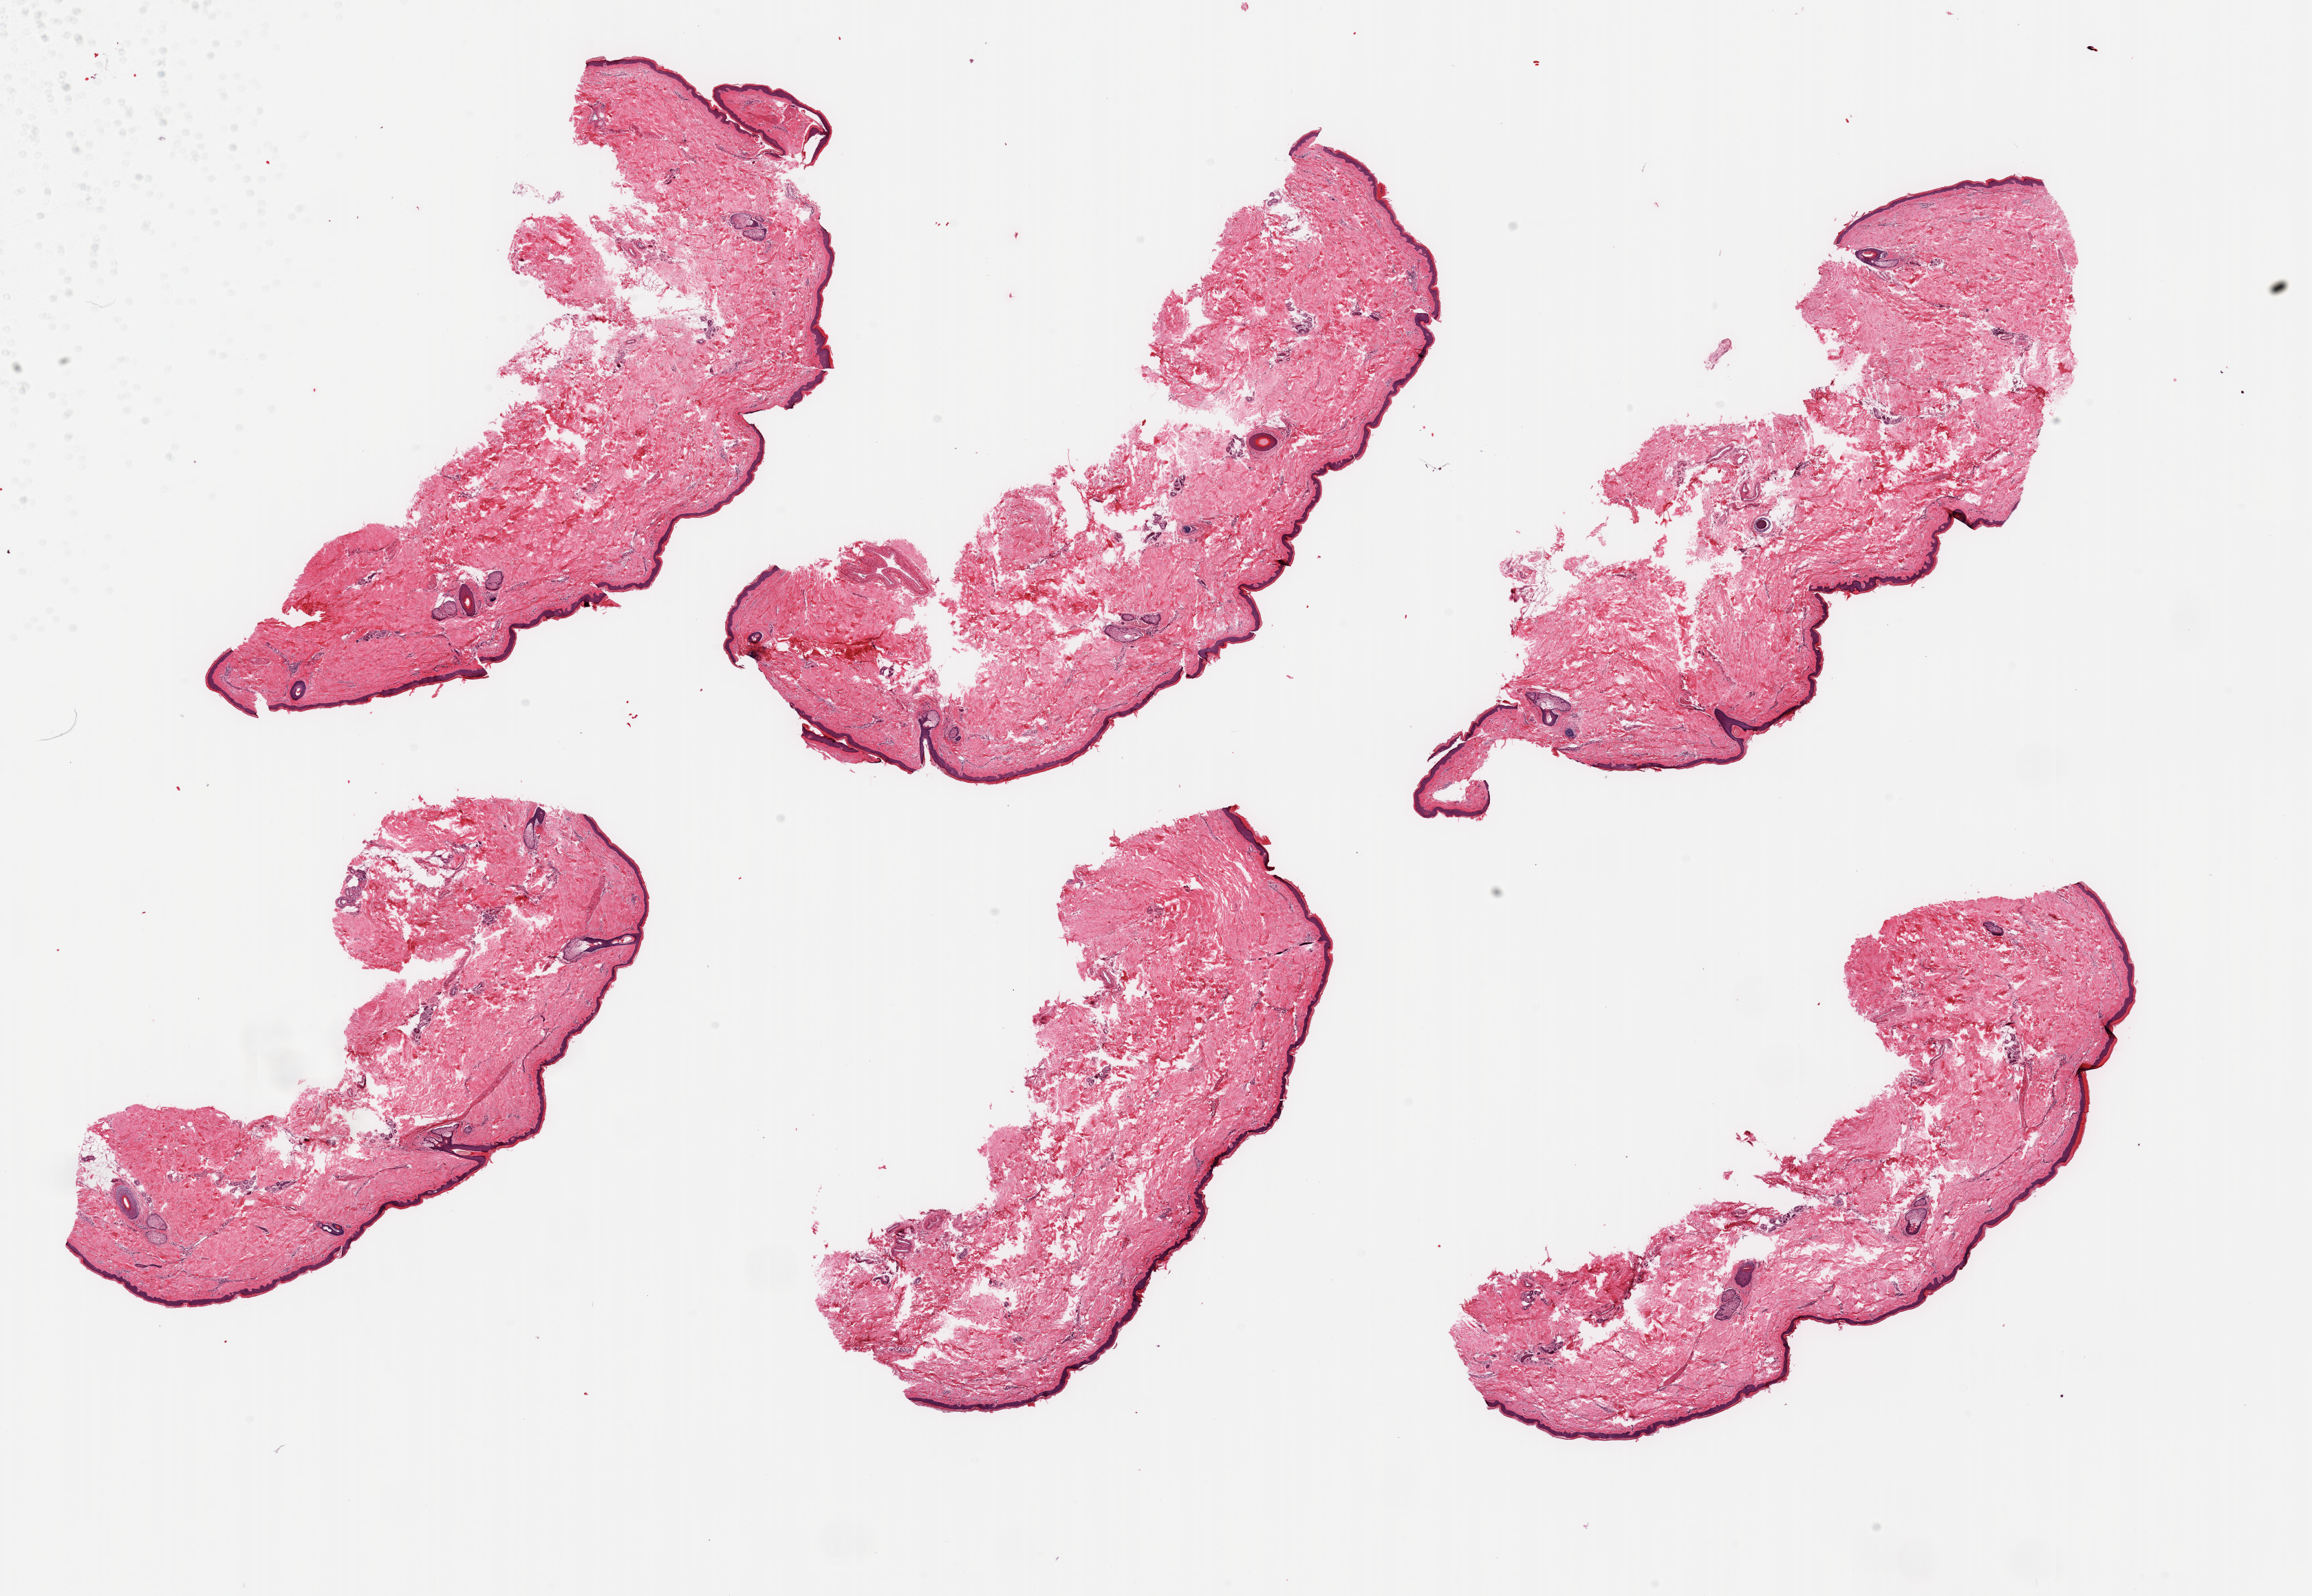
Whole-slide image, hematoxylin and eosin (H&E) stain, brightfield — low-resolution overview of the scanned area, about 26.6 x 18.3 mm; PAXgene-fixed paraffin-embedded (PFPE) section; target tissue: skin of lower leg; donor tissue sample. Donor sex: male.
Review note (as recorded): 6 pieces, minimal dermal fat, squamous epithelium is ~40-50 microns.